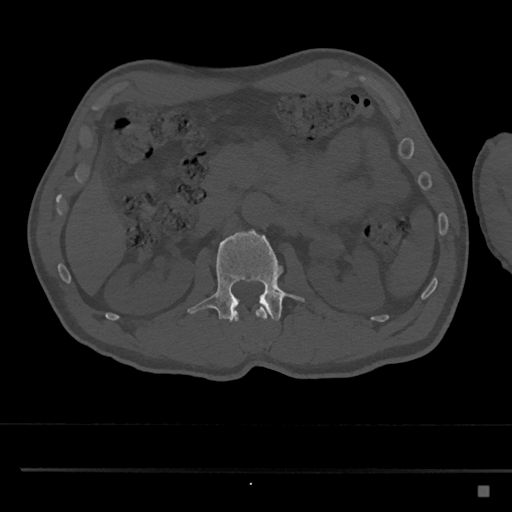
CT including the spine, one axial slice. Slice 776 of 797 in the series (ordered by position). Reconstruction kernel Br40s/3. Bone window (W 1800 / L 400 HU). 0.5 mm slice thickness. 512 × 512 image matrix. Patient: male, 59 years. Case-level facts recorded for this patient, not image findings: primary cancer: prostate.
Structures marked on this image (semi-automatic segmentation, software-assisted and operator-edited):
- L1 vertebra: bounding box (x1, y1, x2, y2) in pixels: (232, 307, 268, 321)
- L2 vertebra: (188, 230, 305, 321)